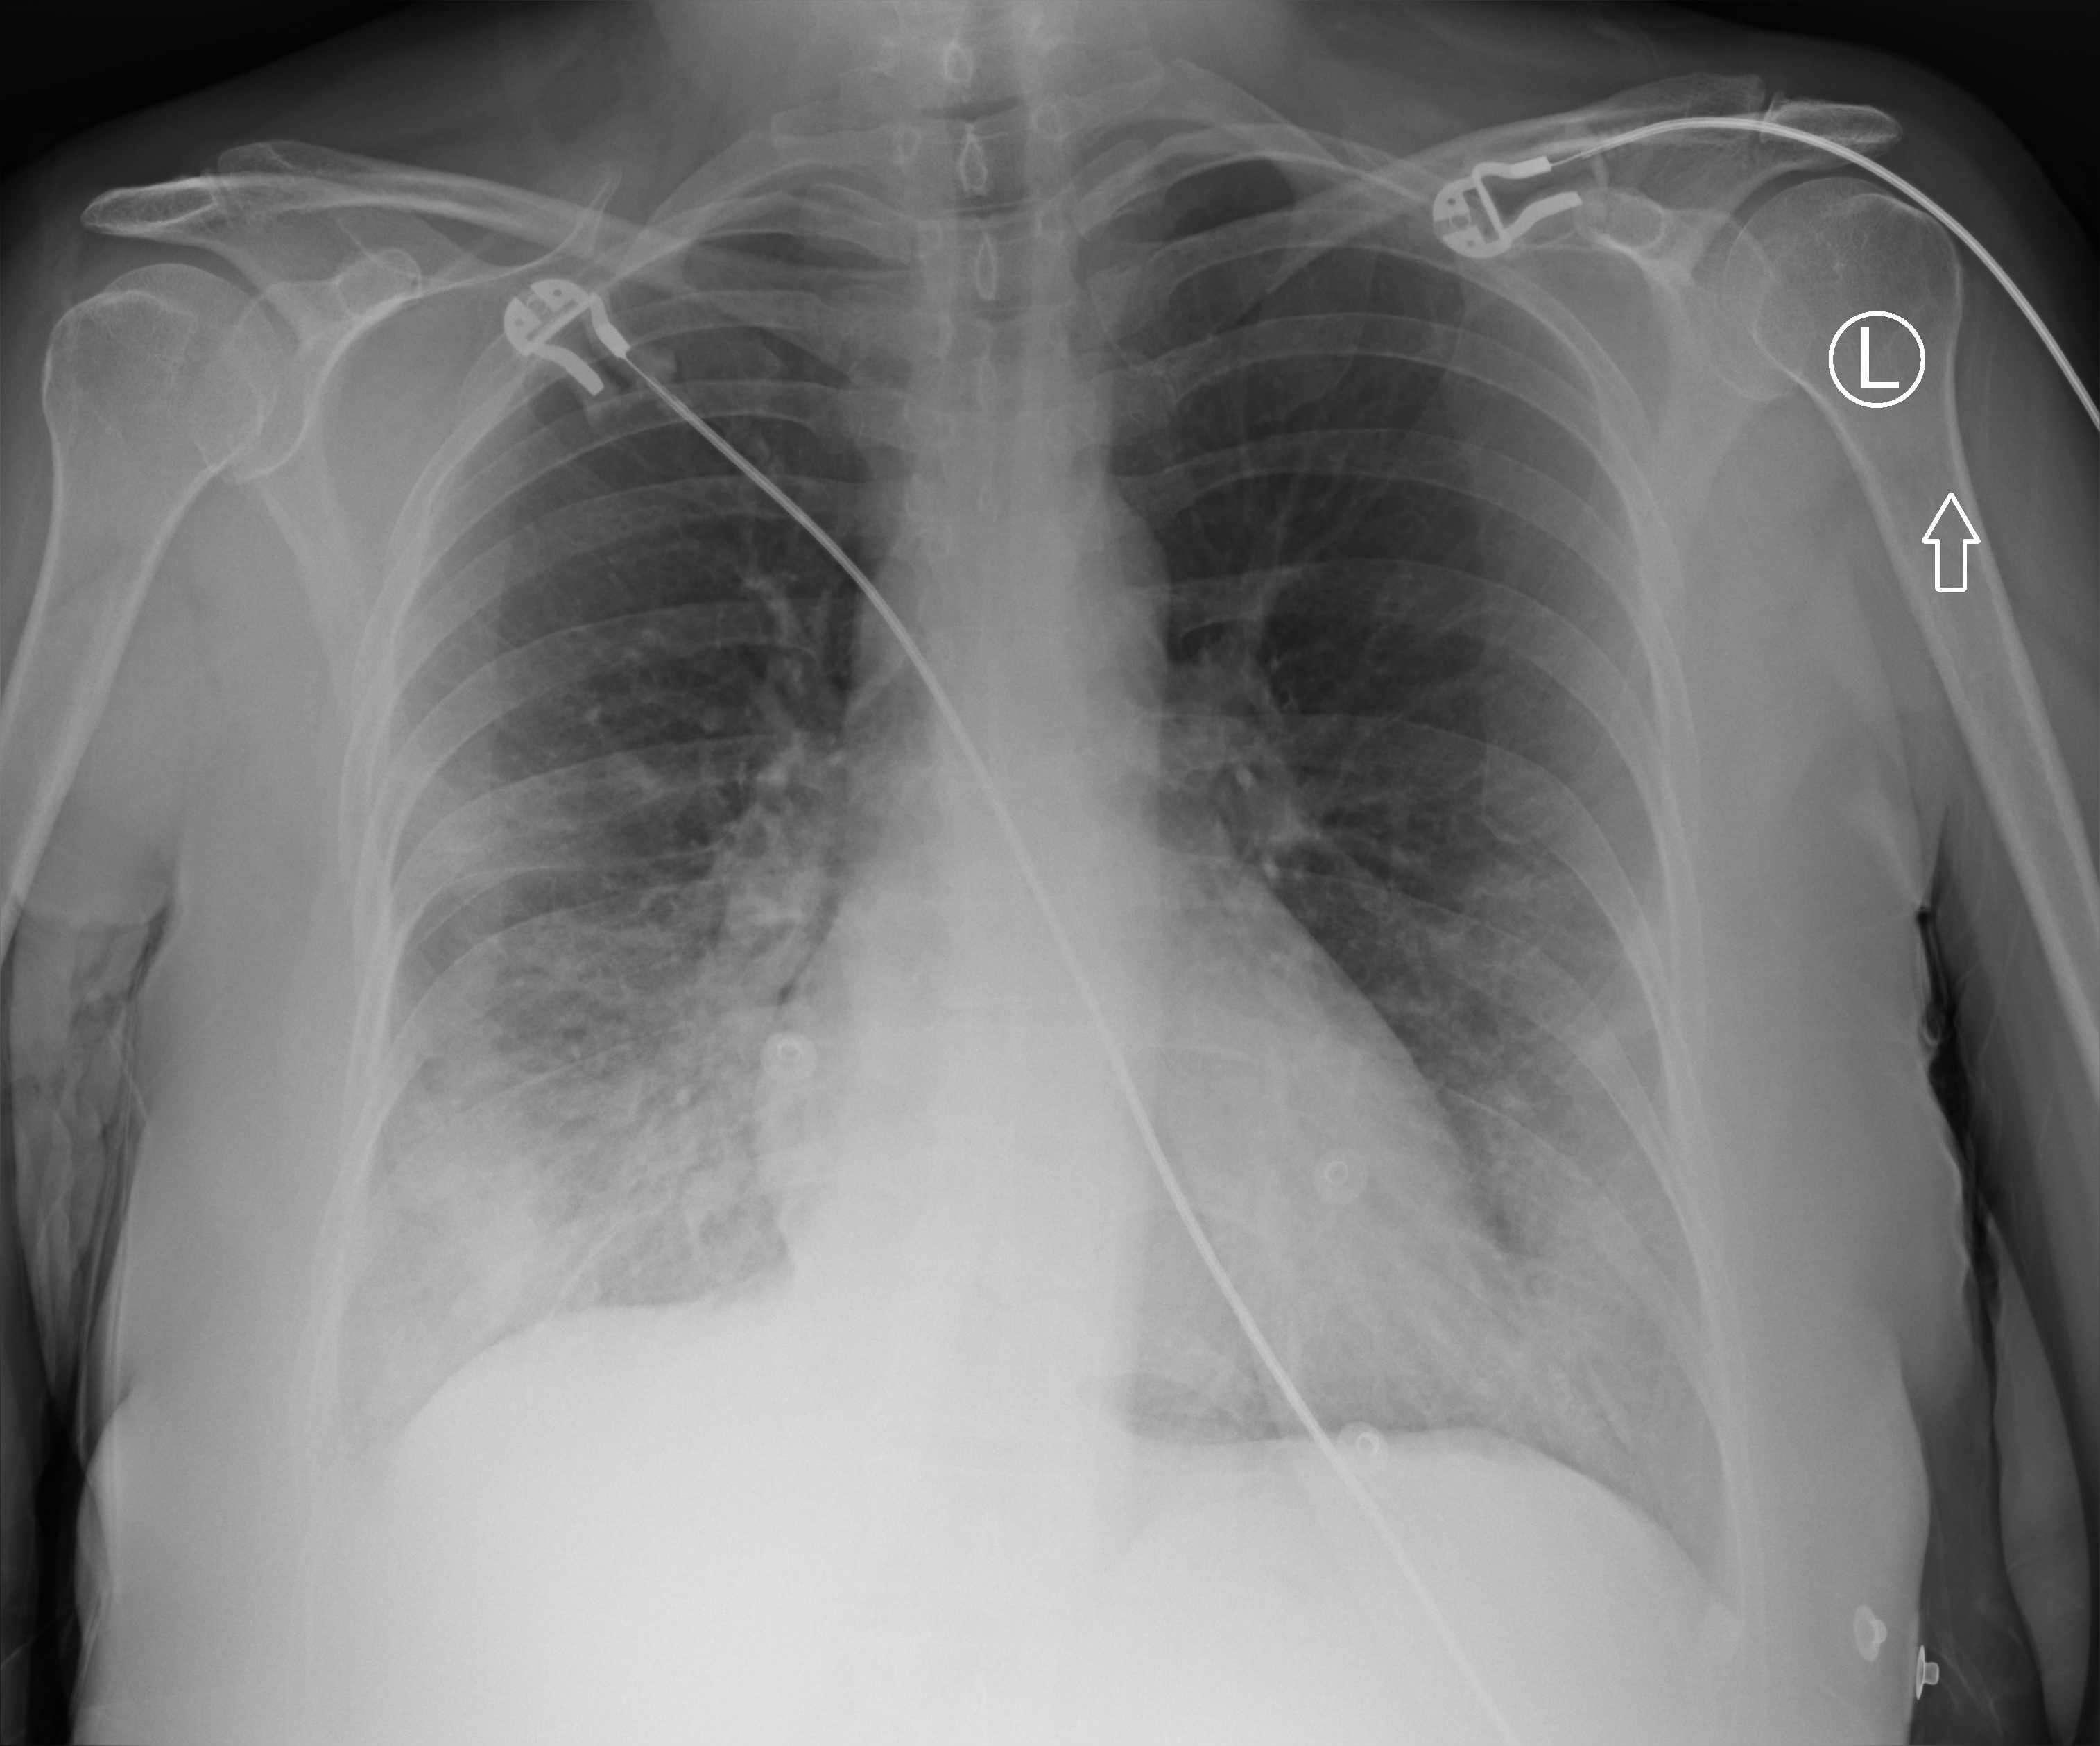
Chest X-ray (portable), anteroposterior (AP) projection. Female patient hospitalised with COVID-19, age 18–59 years.
Hospital-stay facts (about this admission, not read from this image; timing relative to this image not recorded):
- mechanically ventilated during this hospital stay: no